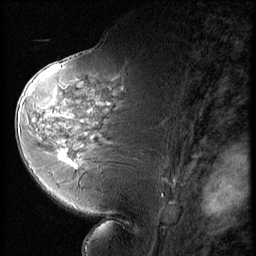
Breast MRI (dynamic contrast-enhanced), one sagittal slice; position 32 of 56 along the scan axis; 3 images stored at this slice position (order not interpretable as contrast timing); 1.5 T; TE 4.2 ms, TR 9 ms; 2.5 mm slice thickness; 256 × 256 image matrix, field of view 180 × 180 mm. Female patient, age 58 years. Case-level facts recorded for this patient, not image findings: setting: breast cancer imaged before/during neoadjuvant chemotherapy; receptor status: HR-positive, HER2-negative.
Annotated regions visible in this slice (semi-automatically segmented with operator editing):
- analysis volume of interest (the breast-tissue region the enhancement analysis was run in; not a lesion): bounding box (x1, y1, x2, y2) in pixels: (47, 136, 88, 178)
- tumour enhancement mask (voxels above the 140 % enhancement threshold inside the analysis volume of interest): (58, 150, 77, 166)